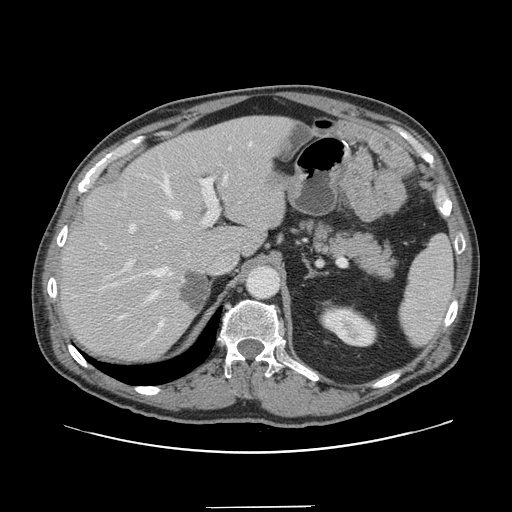
Contrast-enhanced abdominal CT, one axial slice. Position 102 of 139 along the scan axis. 120 kVp. Intravenous contrast given. Soft-tissue window (W 400 / L 40 HU). 2.5 mm slice thickness. 512 × 512 image matrix, field of view 397 × 397 mm. Male patient, age 64 years. From the clinical record (not read from this slice): diagnosis: colorectal cancer liver metastases, imaged before liver resection; multiple liver metastases: yes.
Structures marked on this image (manually delineated by an expert):
- hepatic veins: box from (x=104, y=142) to (x=252, y=339) px
- liver: (x=61, y=117)–(x=292, y=360)
- planned liver remnant (the part of the liver to remain after resection): (x=61, y=117)–(x=276, y=360)
- portal vein (with intrahepatic branches): (x=119, y=147)–(x=231, y=273)
- liver metastasis: (x=181, y=272)–(x=206, y=311)